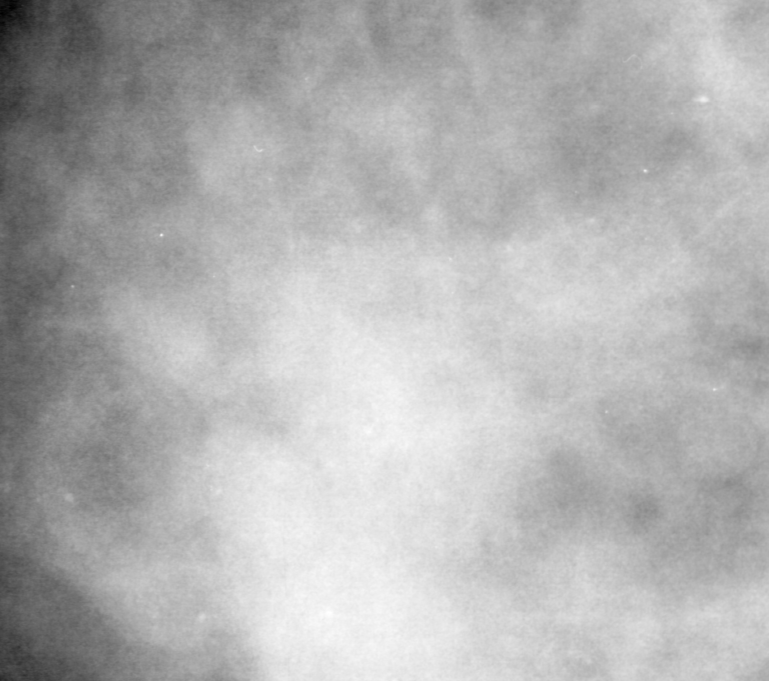
Crop from a digitized film mammogram around one marked abnormality, left breast, CC view, BI-RADS breast density category 4 (scale 1–4).
- Calcifications, morphology punctate, distribution segmental; BI-RADS assessment category 4; pathology (as recorded): malignant.